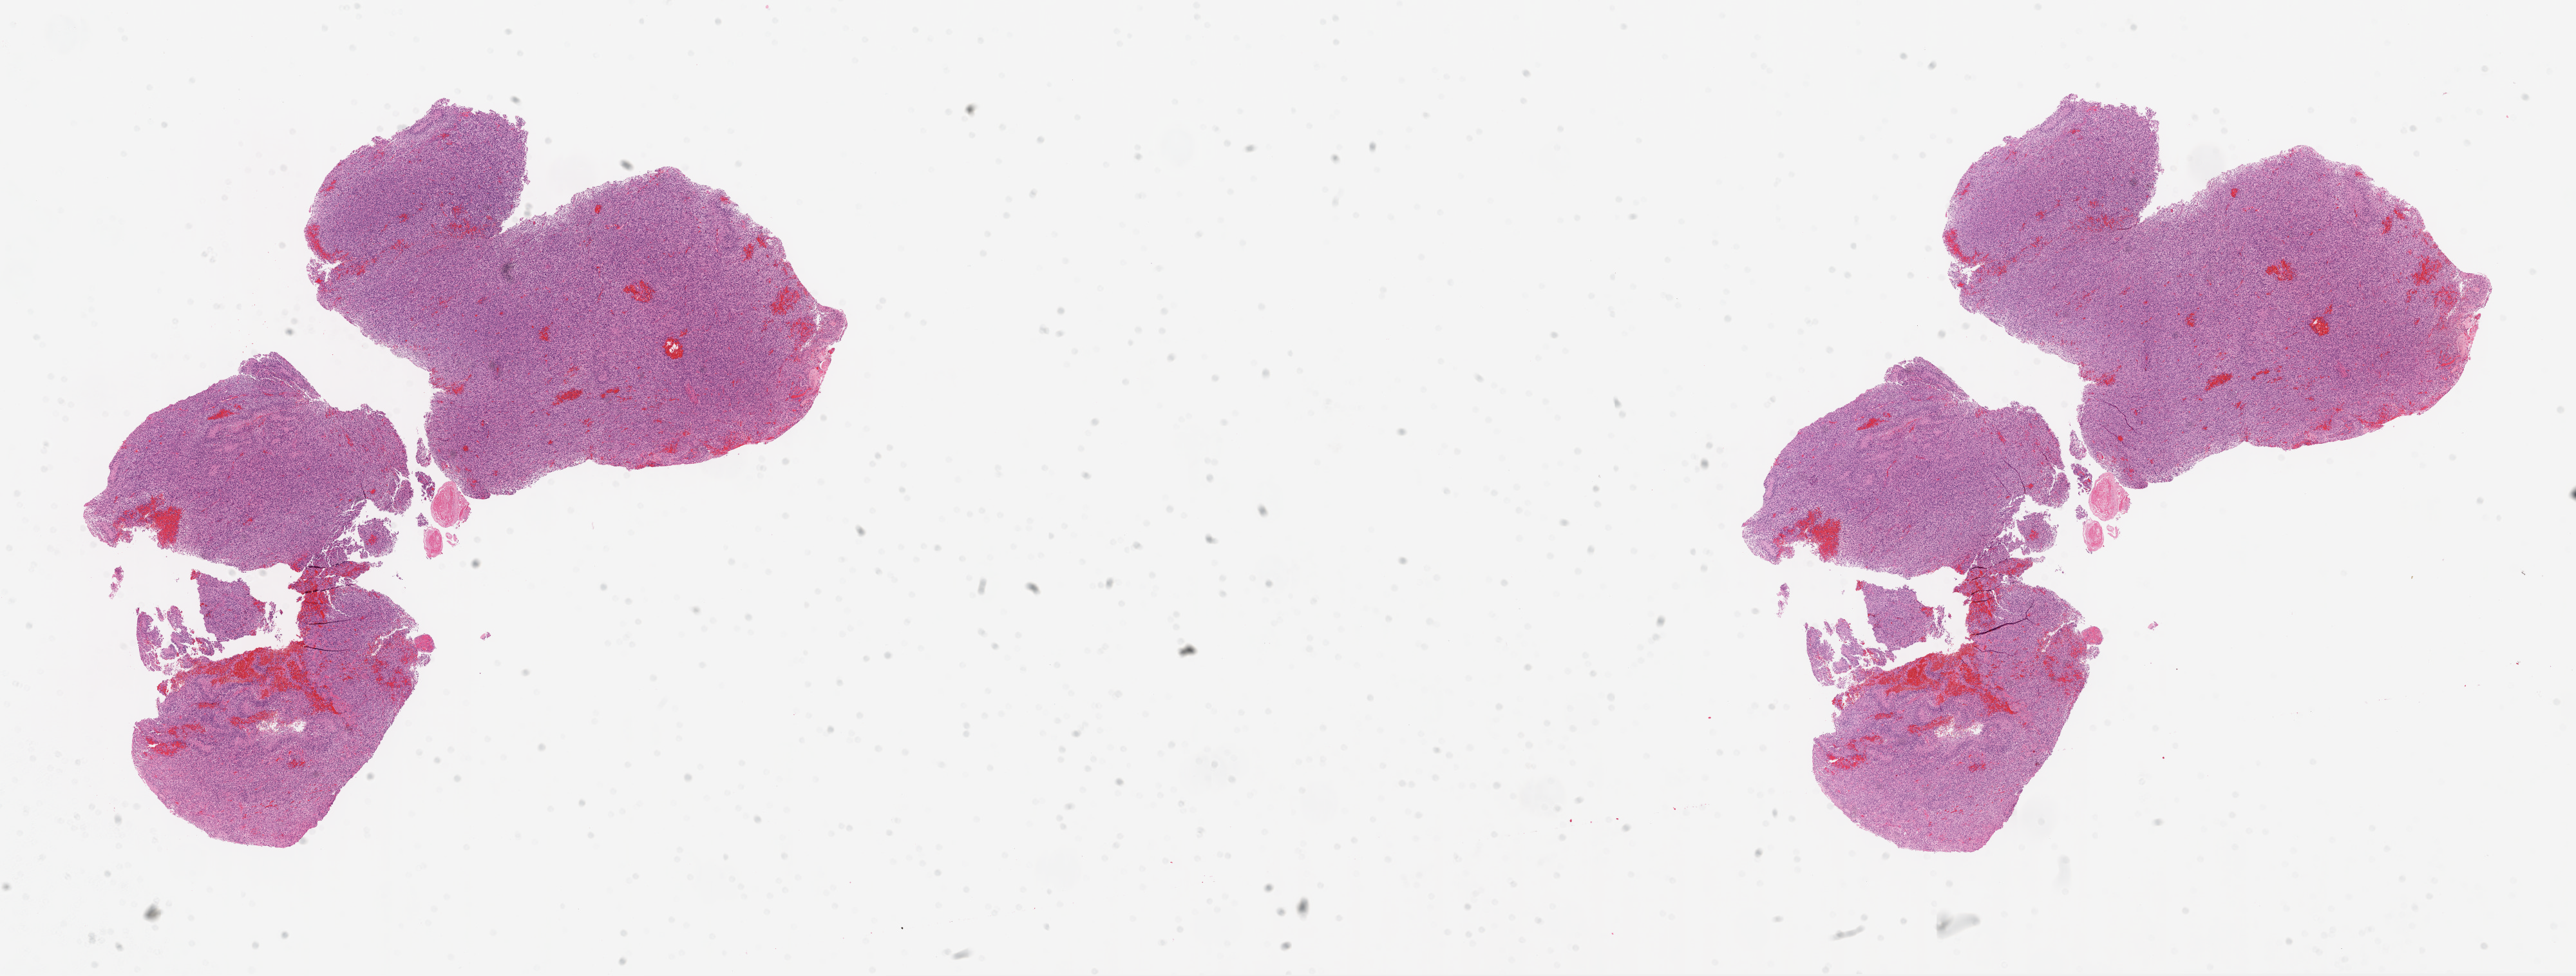
Digitized H&E tissue section (whole slide), low-resolution overview of the scanned area, about 32.1 x 12.2 mm (acquisition: 20x scan), frozen section from the top of the tissue portion, brain, primary tumour sample. Male patient; age at initial diagnosis 72 years. Pathologist review of this section (percent, as recorded): tumour cells 95%, tumour nuclei 85%, normal cells 0%, stromal cells 0%, necrosis 5%.
- histologic diagnosis: Glioblastoma